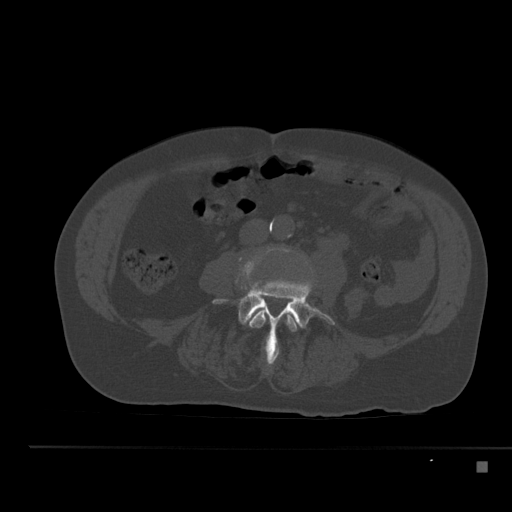
CT including the spine, one axial slice; position 149 of 517 along the scan axis; reconstruction kernel Br40s; 120 kVp; bone window (W 1800 / L 400 HU); 512 × 512 image matrix. Male patient, age 70 years. From the clinical record (not read from this slice): primary cancer: renal.
Outlined on this slice (semi-automatically segmented with operator editing):
- L3 vertebra: bounding box (x1, y1, x2, y2) in pixels: (235, 253, 298, 362)
- L4 vertebra: (213, 276, 335, 366)